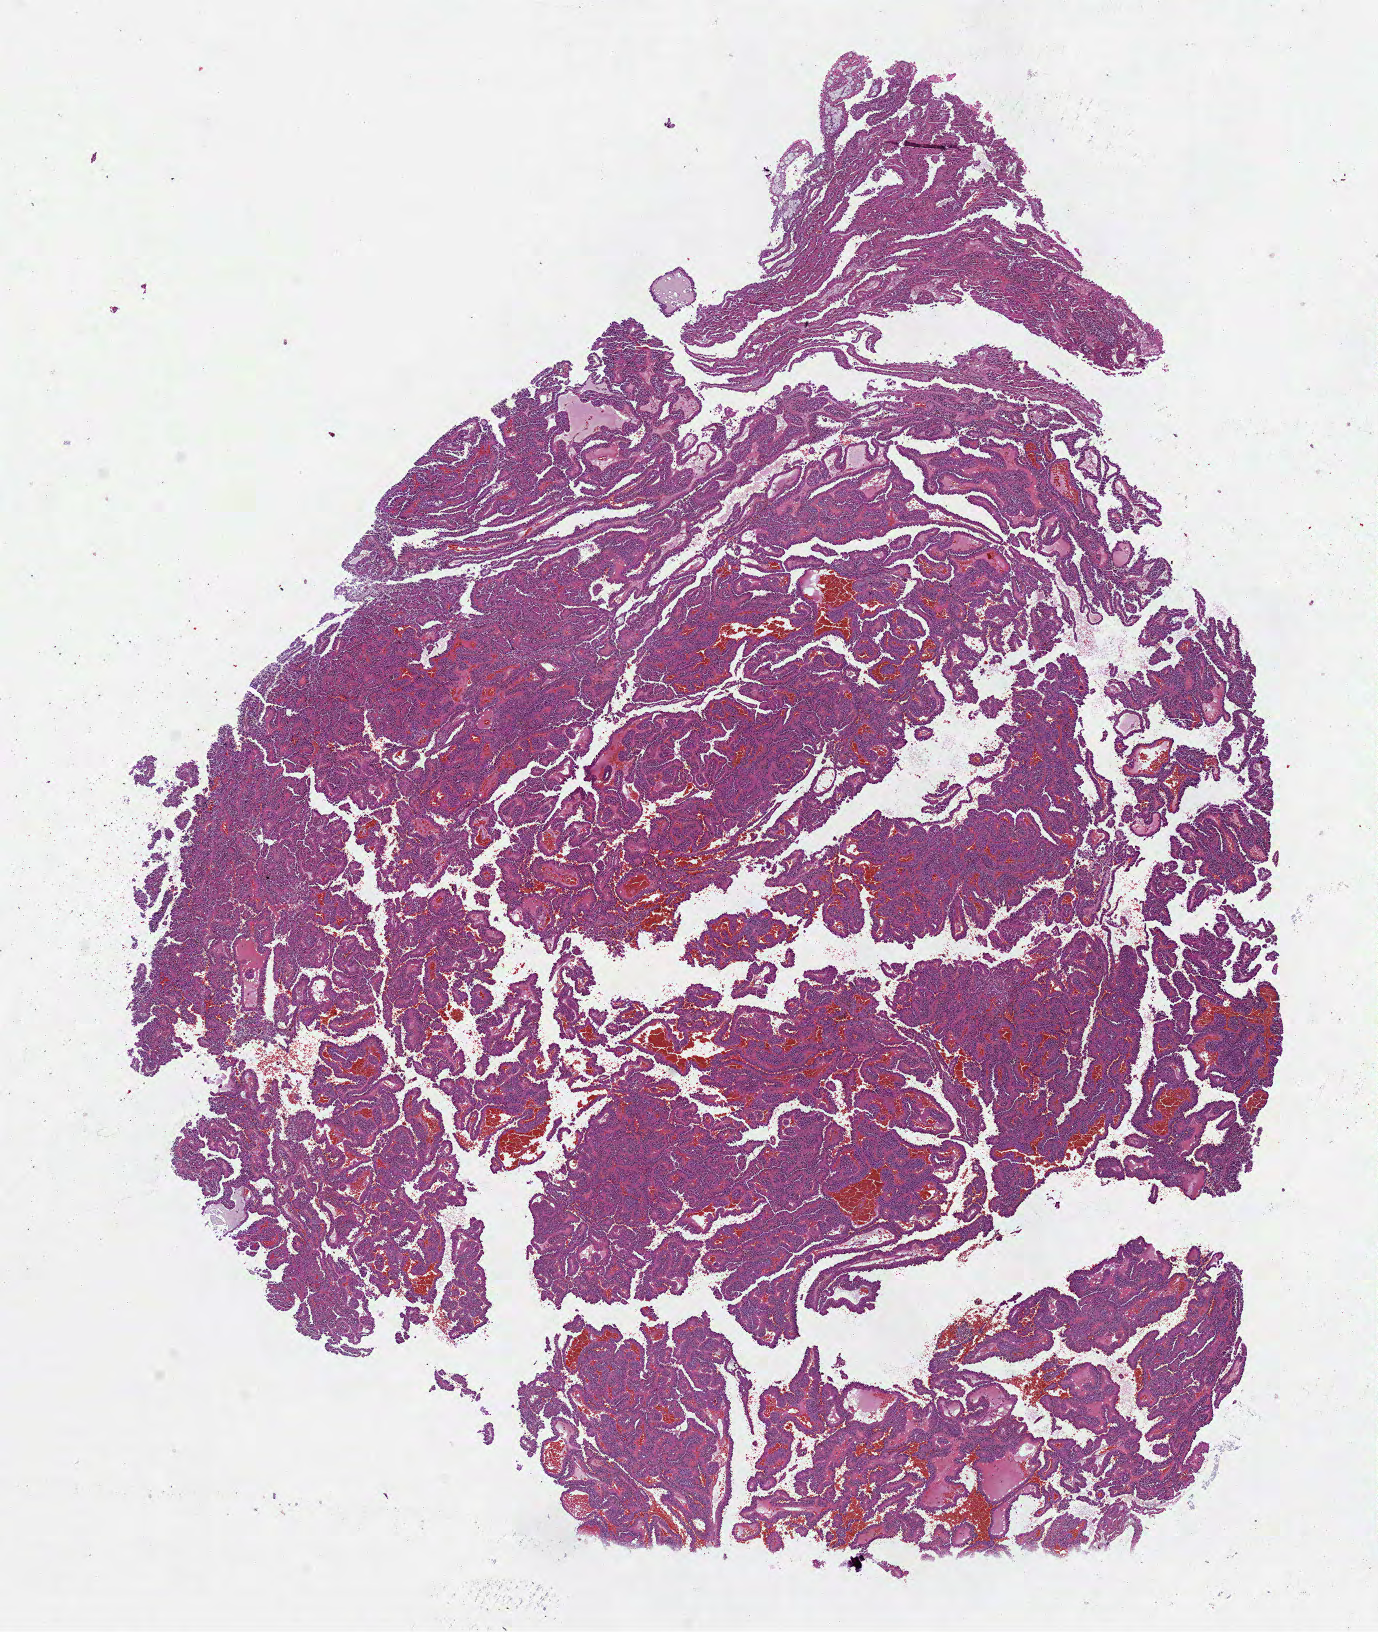
H&E-stained whole-slide image — low-resolution overview of the scanned area, about 11.1 x 13.2 mm (from a 40x scan); formalin-fixed paraffin-embedded (FFPE) diagnostic section; kidney, primary tumour sample. Female patient; age at initial diagnosis 61 years.
AJCC pathologic stage: I. TNM: T1b NX MX. Laterality: left. Diagnosis: Papillary adenocarcinoma, NOS.